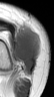
MRI of an extremity soft-tissue mass, one axial slice; position 19 of 42 along the scan axis; MR volume resampled by the dataset authors to the PET/CT grid (not the native acquisition matrix); 3.27 mm slice thickness; 54 × 97 image matrix. Female patient. From the clinical record (not read from this slice): histological type: spindle cell suggestive of biphasic synovial sarcoma; grade: intermediate; site of the primary tumour: left knee.
Outlined on this slice (expert contour drawn on MRI and transferred to this co-registered scan by the dataset authors):
- gross tumour volume including surrounding oedema: bounding box (x1, y1, x2, y2) in pixels: (14, 26, 38, 75)
- gross tumour volume (mass): (14, 28, 38, 75)